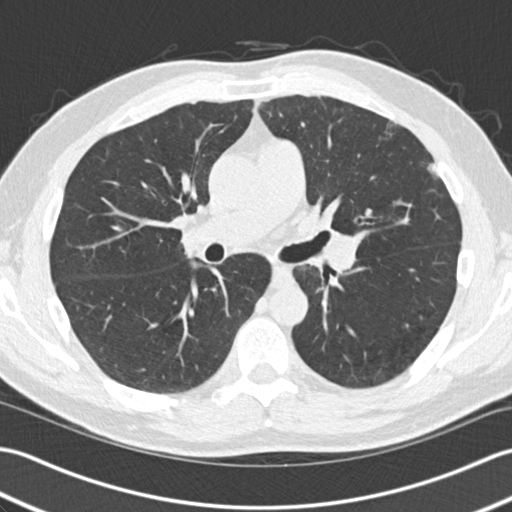
Low-dose screening chest CT, one axial slice; reconstruction kernel B30f; lung window (W 1500 / L -600 HU); 2 mm slice thickness; 512 × 512 image matrix.
Annotated regions visible in this slice (outlined manually by an expert reader):
- lesion 1 (tumor, upper lobe of left lung): bounding box [x1, y1, x2, y2] px = [427, 163, 440, 178]